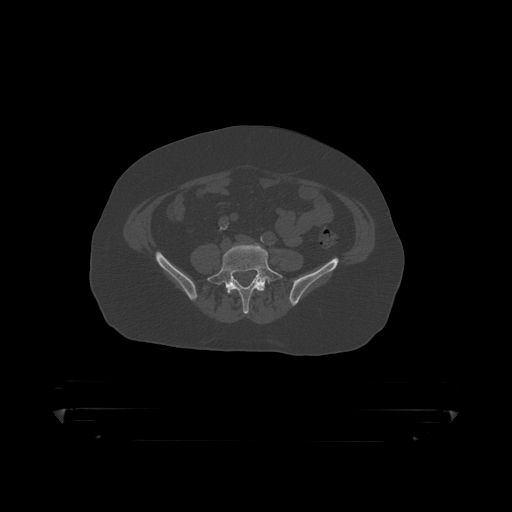
CT including the spine, one axial slice; slice 43 of 390 in the series (ordered by position); reconstruction kernel STANDARD; 120 kVp; bone window (W 1800 / L 400 HU); 1.25 mm slice thickness; 512 × 512 image matrix, field of view 650 × 650 mm. Patient: male, 60 years. From the clinical record (not read from this slice): primary cancer: prostate.
Structures marked on this image (semi-automatically segmented with operator editing):
- L4 vertebra: bounding box <227,283,265,295> (left, top, right, bottom; pixels)
- L5 vertebra: <208,245,284,314>